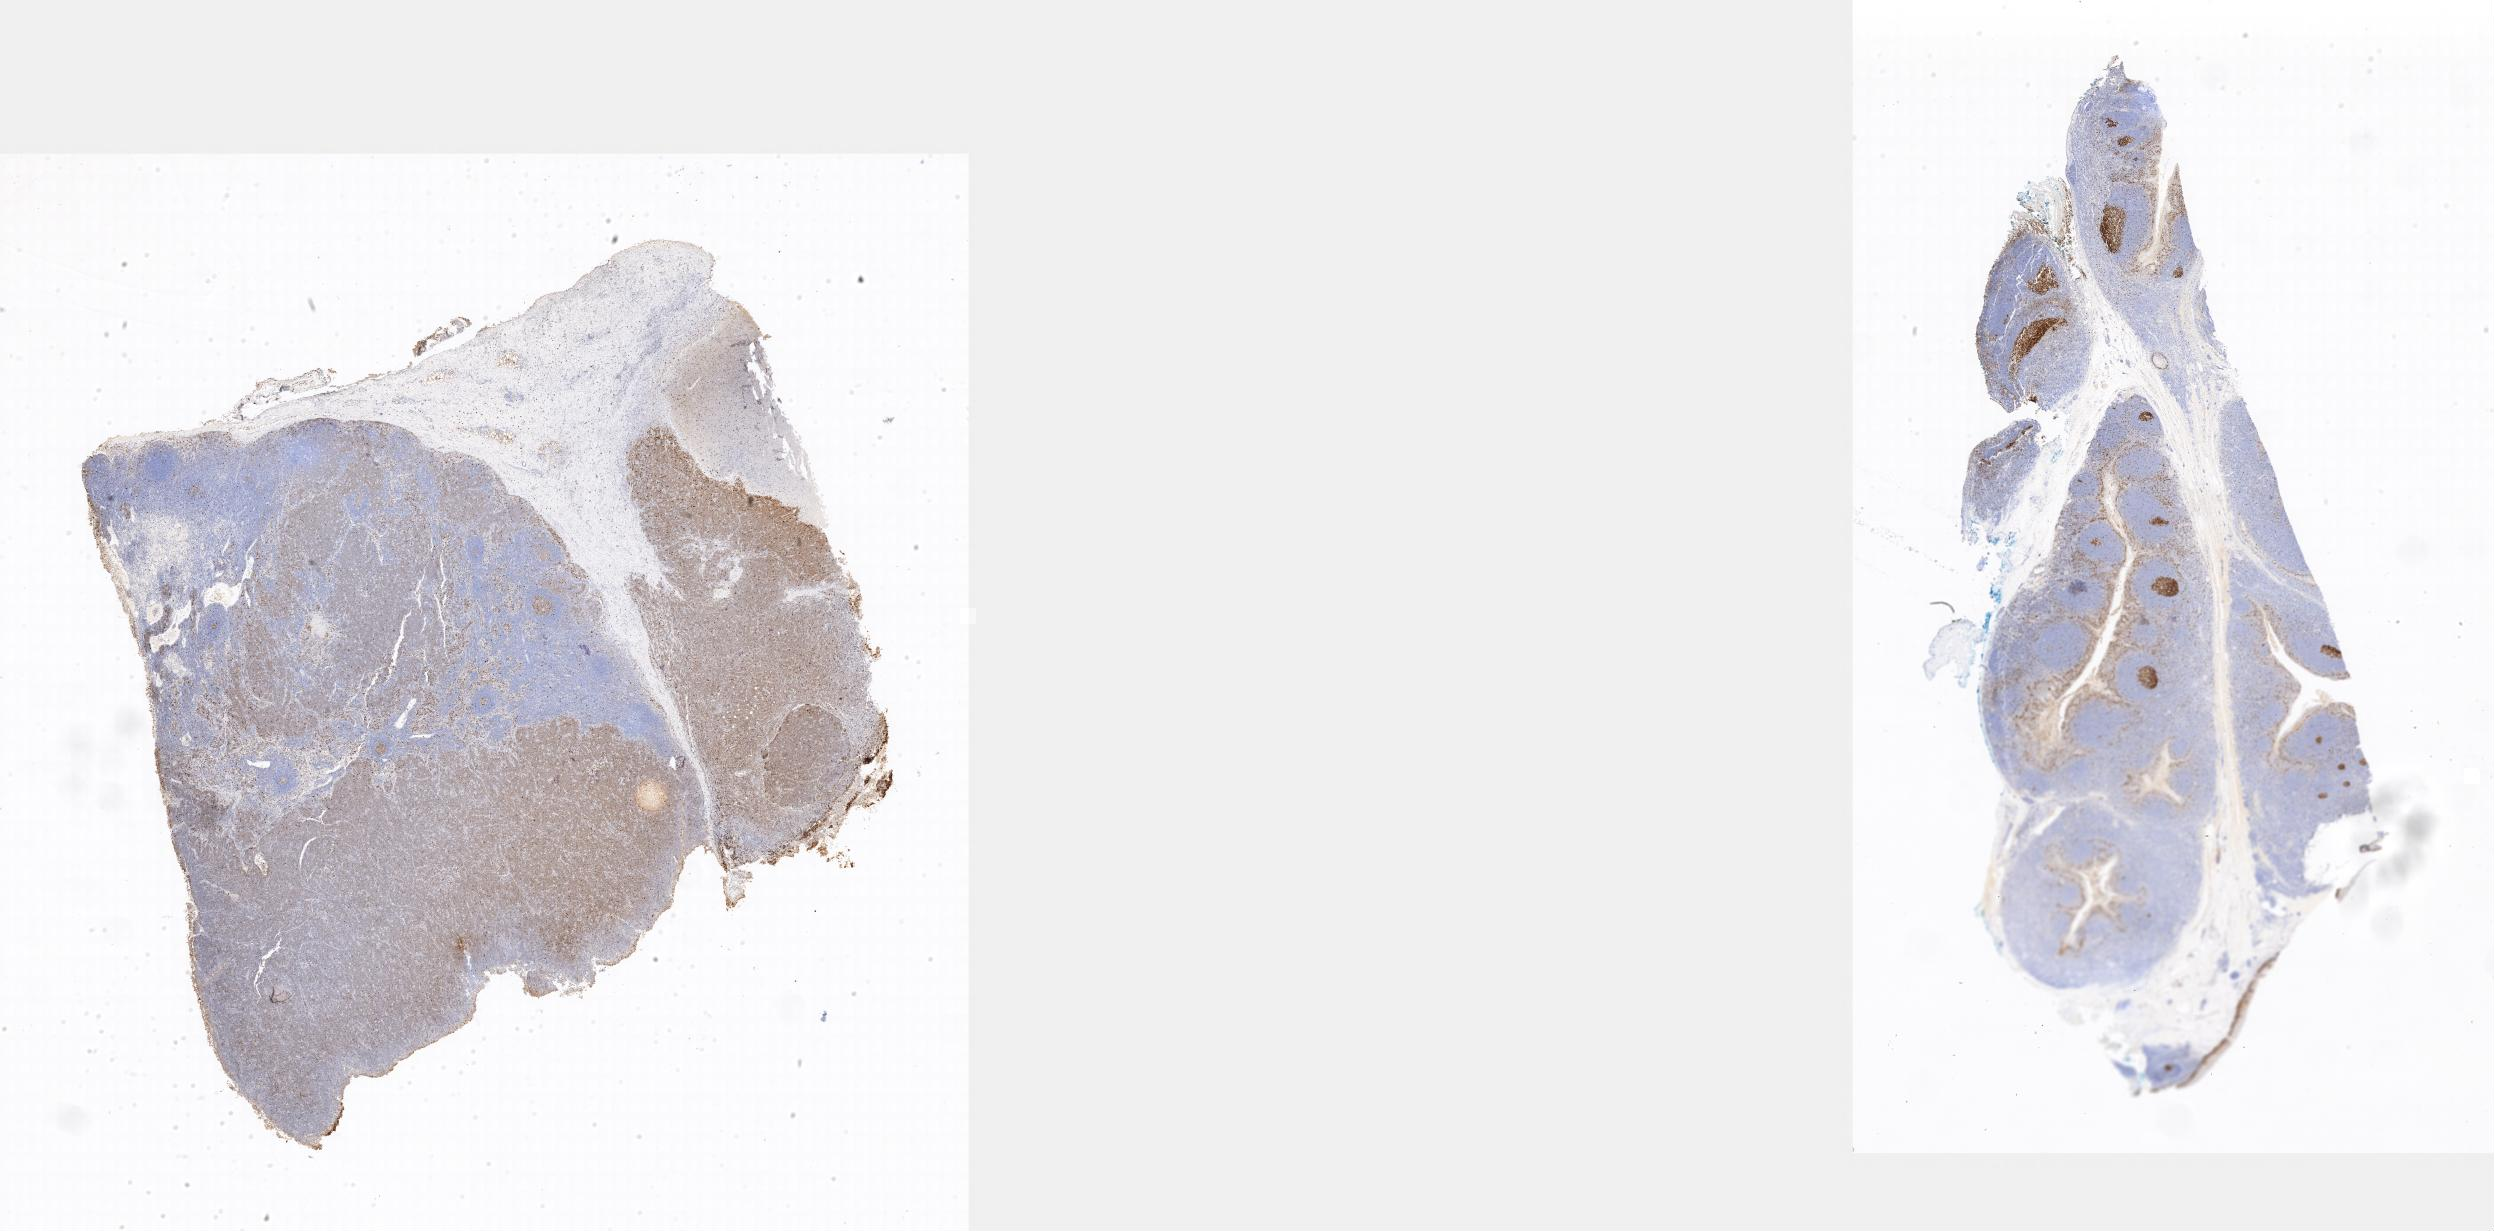
Whole-slide image, immunohistochemical stain for Ki-67 — a low-resolution overview of the entire scanned area. Tumor tissue. Site: abdominal lymph node. Female patient, age 14 years.
• histologic diagnosis: Burkitt lymphoma, NOS